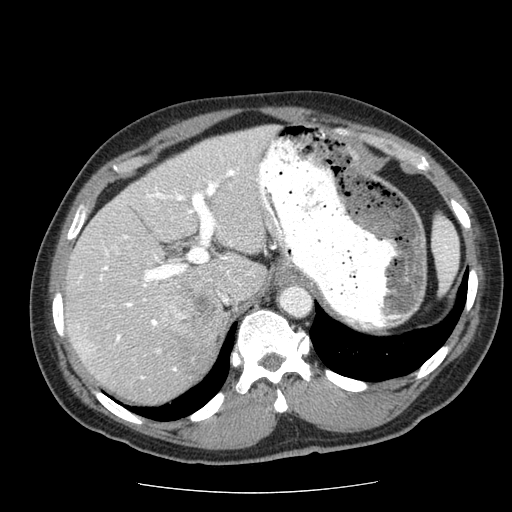
Contrast-enhanced abdominal CT (liver protocol), one axial slice. Slice 42 of 85 in the series (ordered by position). Reconstruction kernel STANDARD. 120 kVp. Soft-tissue window (W 400 / L 40 HU). 2.5 mm slice thickness. 512 × 512 image matrix, field of view 360 × 360 mm. Case-level facts recorded for this patient, not image findings: diagnosis: hepatocellular carcinoma (patient treated with transarterial chemoembolisation; whether this scan precedes or follows treatment is not stated here); TNM stage (as recorded): Stage-IIIA; Child-Pugh class: A; tumour differentiation: well differentiated.
Outlined on this slice (semi-automatic segmentation, software-assisted and operator-edited):
- liver parenchyma outside the tumour (the mass and vessels are separate outlines, so this box may not span the whole liver): bounding box [x1, y1, x2, y2] px = [64, 126, 276, 404]
- mass: [159, 290, 226, 341]
- liver vessels: [75, 168, 238, 379]